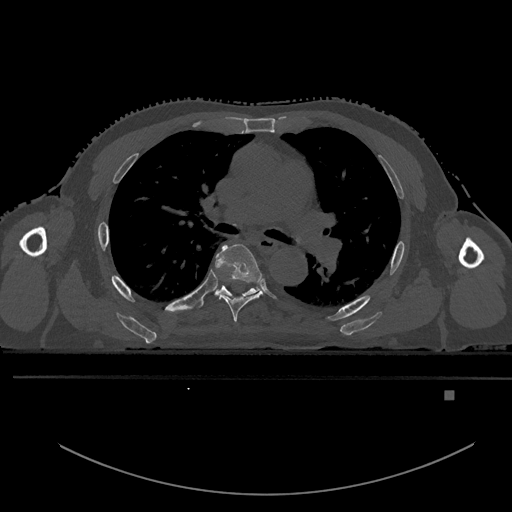
CT including the spine, one axial slice. Position 340 of 969 along the scan axis. Bone window (W 1800 / L 400 HU). 512 × 512 image matrix. Male patient, age 82 years. From the clinical record (not read from this slice): primary cancer: prostate.
Annotated regions visible in this slice (semi-automatically segmented with operator editing):
- T5 vertebra: bounding box [x1, y1, x2, y2] px = [214, 244, 263, 322]
- T6 vertebra: [198, 279, 260, 307]